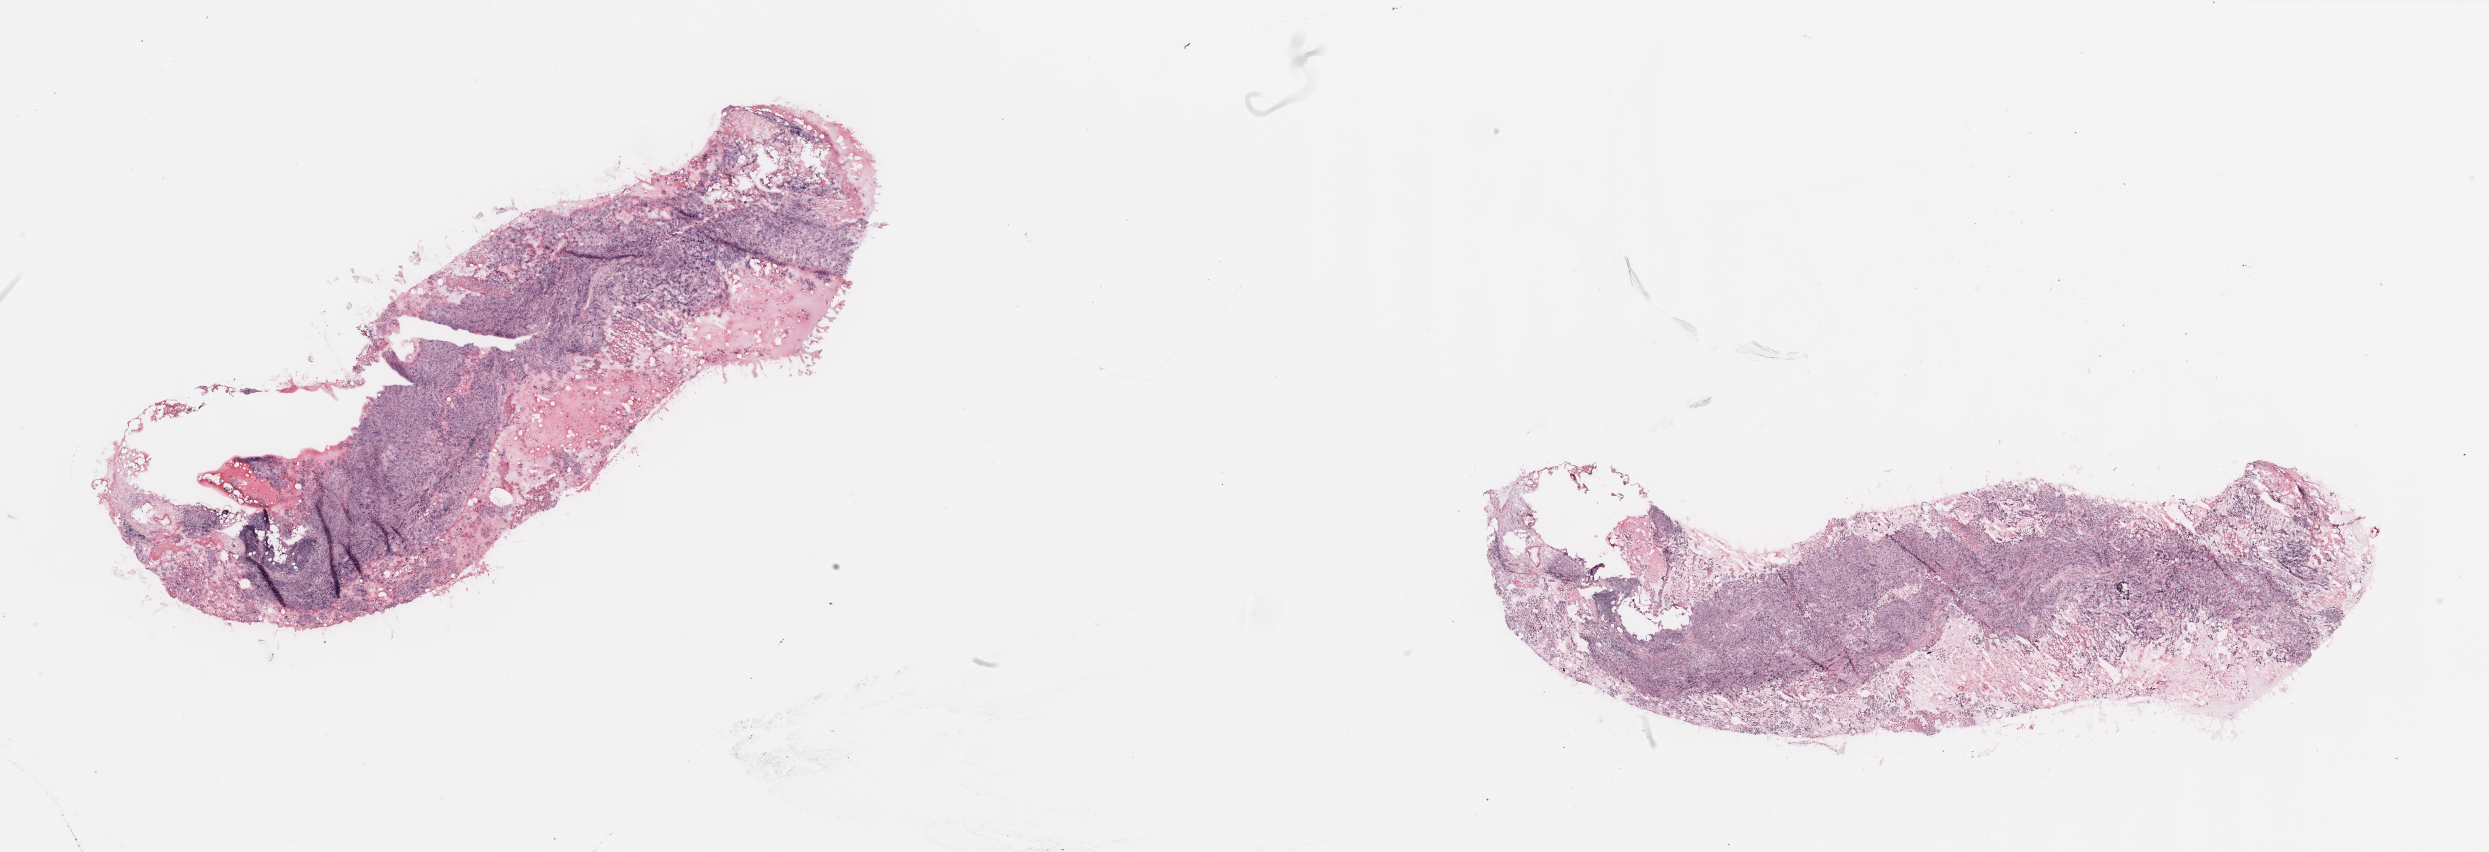
Digitized Hematoxylin and eosin (H&E) stained tissue section (whole slide) — a low-resolution overview of the entire scanned area, about 39.4 x 13.5 mm; breast, tissue type not recorded.
- patient diagnosis (cohort enrolment): breast cancer (breast)